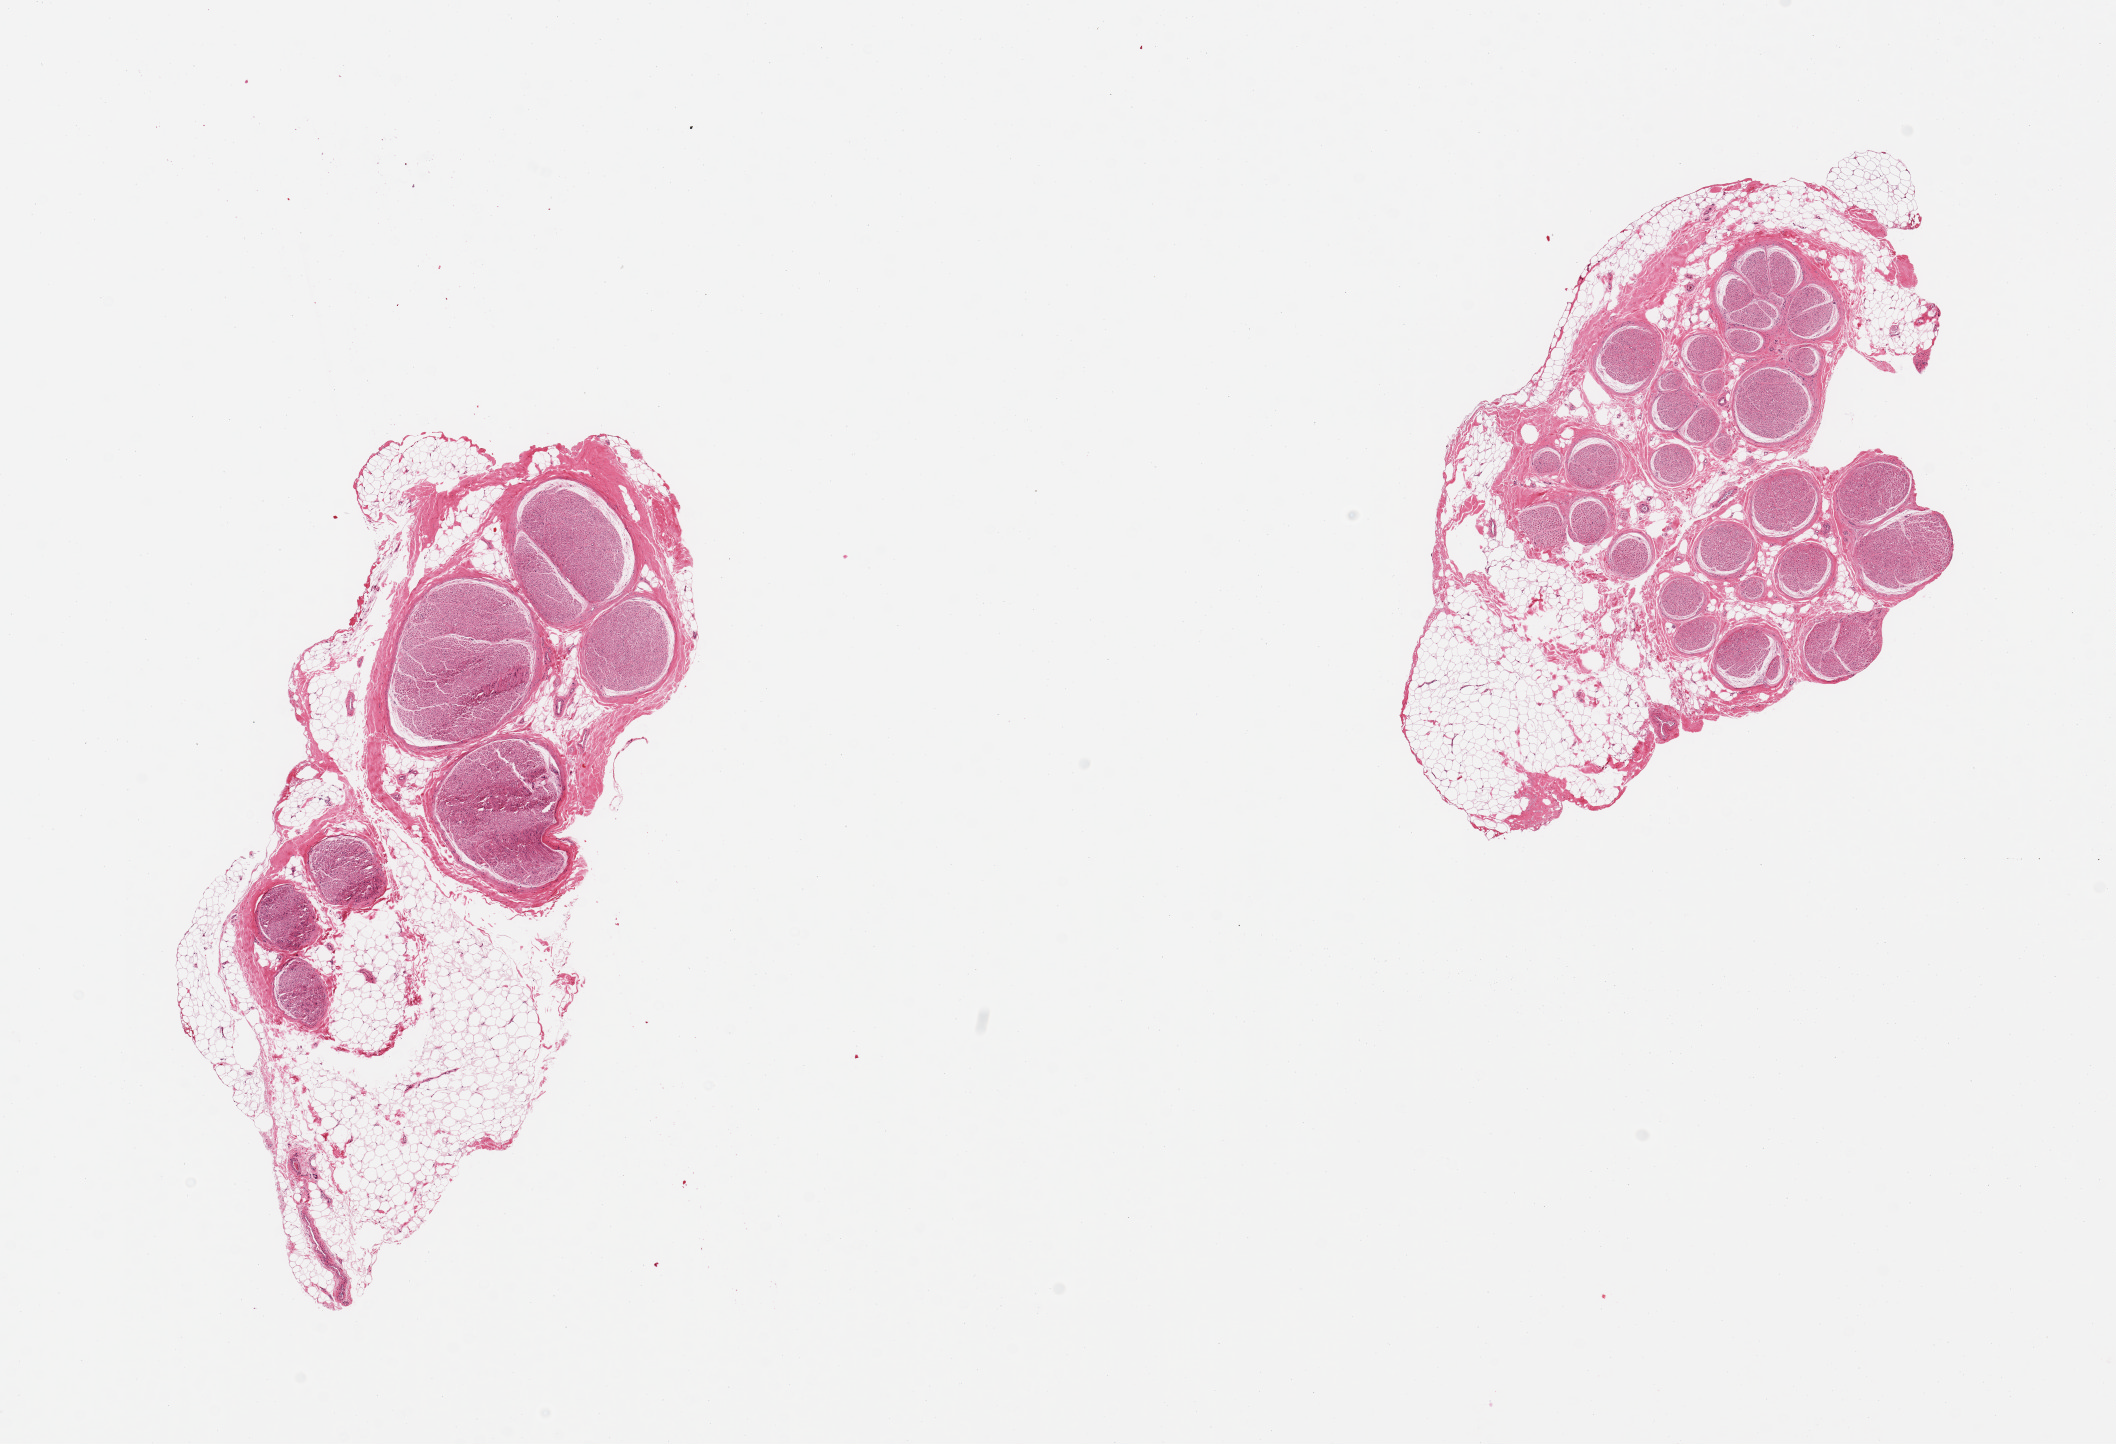
Digitized hematoxylin and eosin (H&E)-stained section, brightfield, low-resolution overview of the scanned area, about 16.7 x 11.4 mm. PAXgene-fixed, paraffin-embedded tissue. Target tissue: tibial nerve. Tissue donor sample. Donor: female.
Reviewer comment on this tissue sample: 2 pieces; include ~50% internal/external fat.